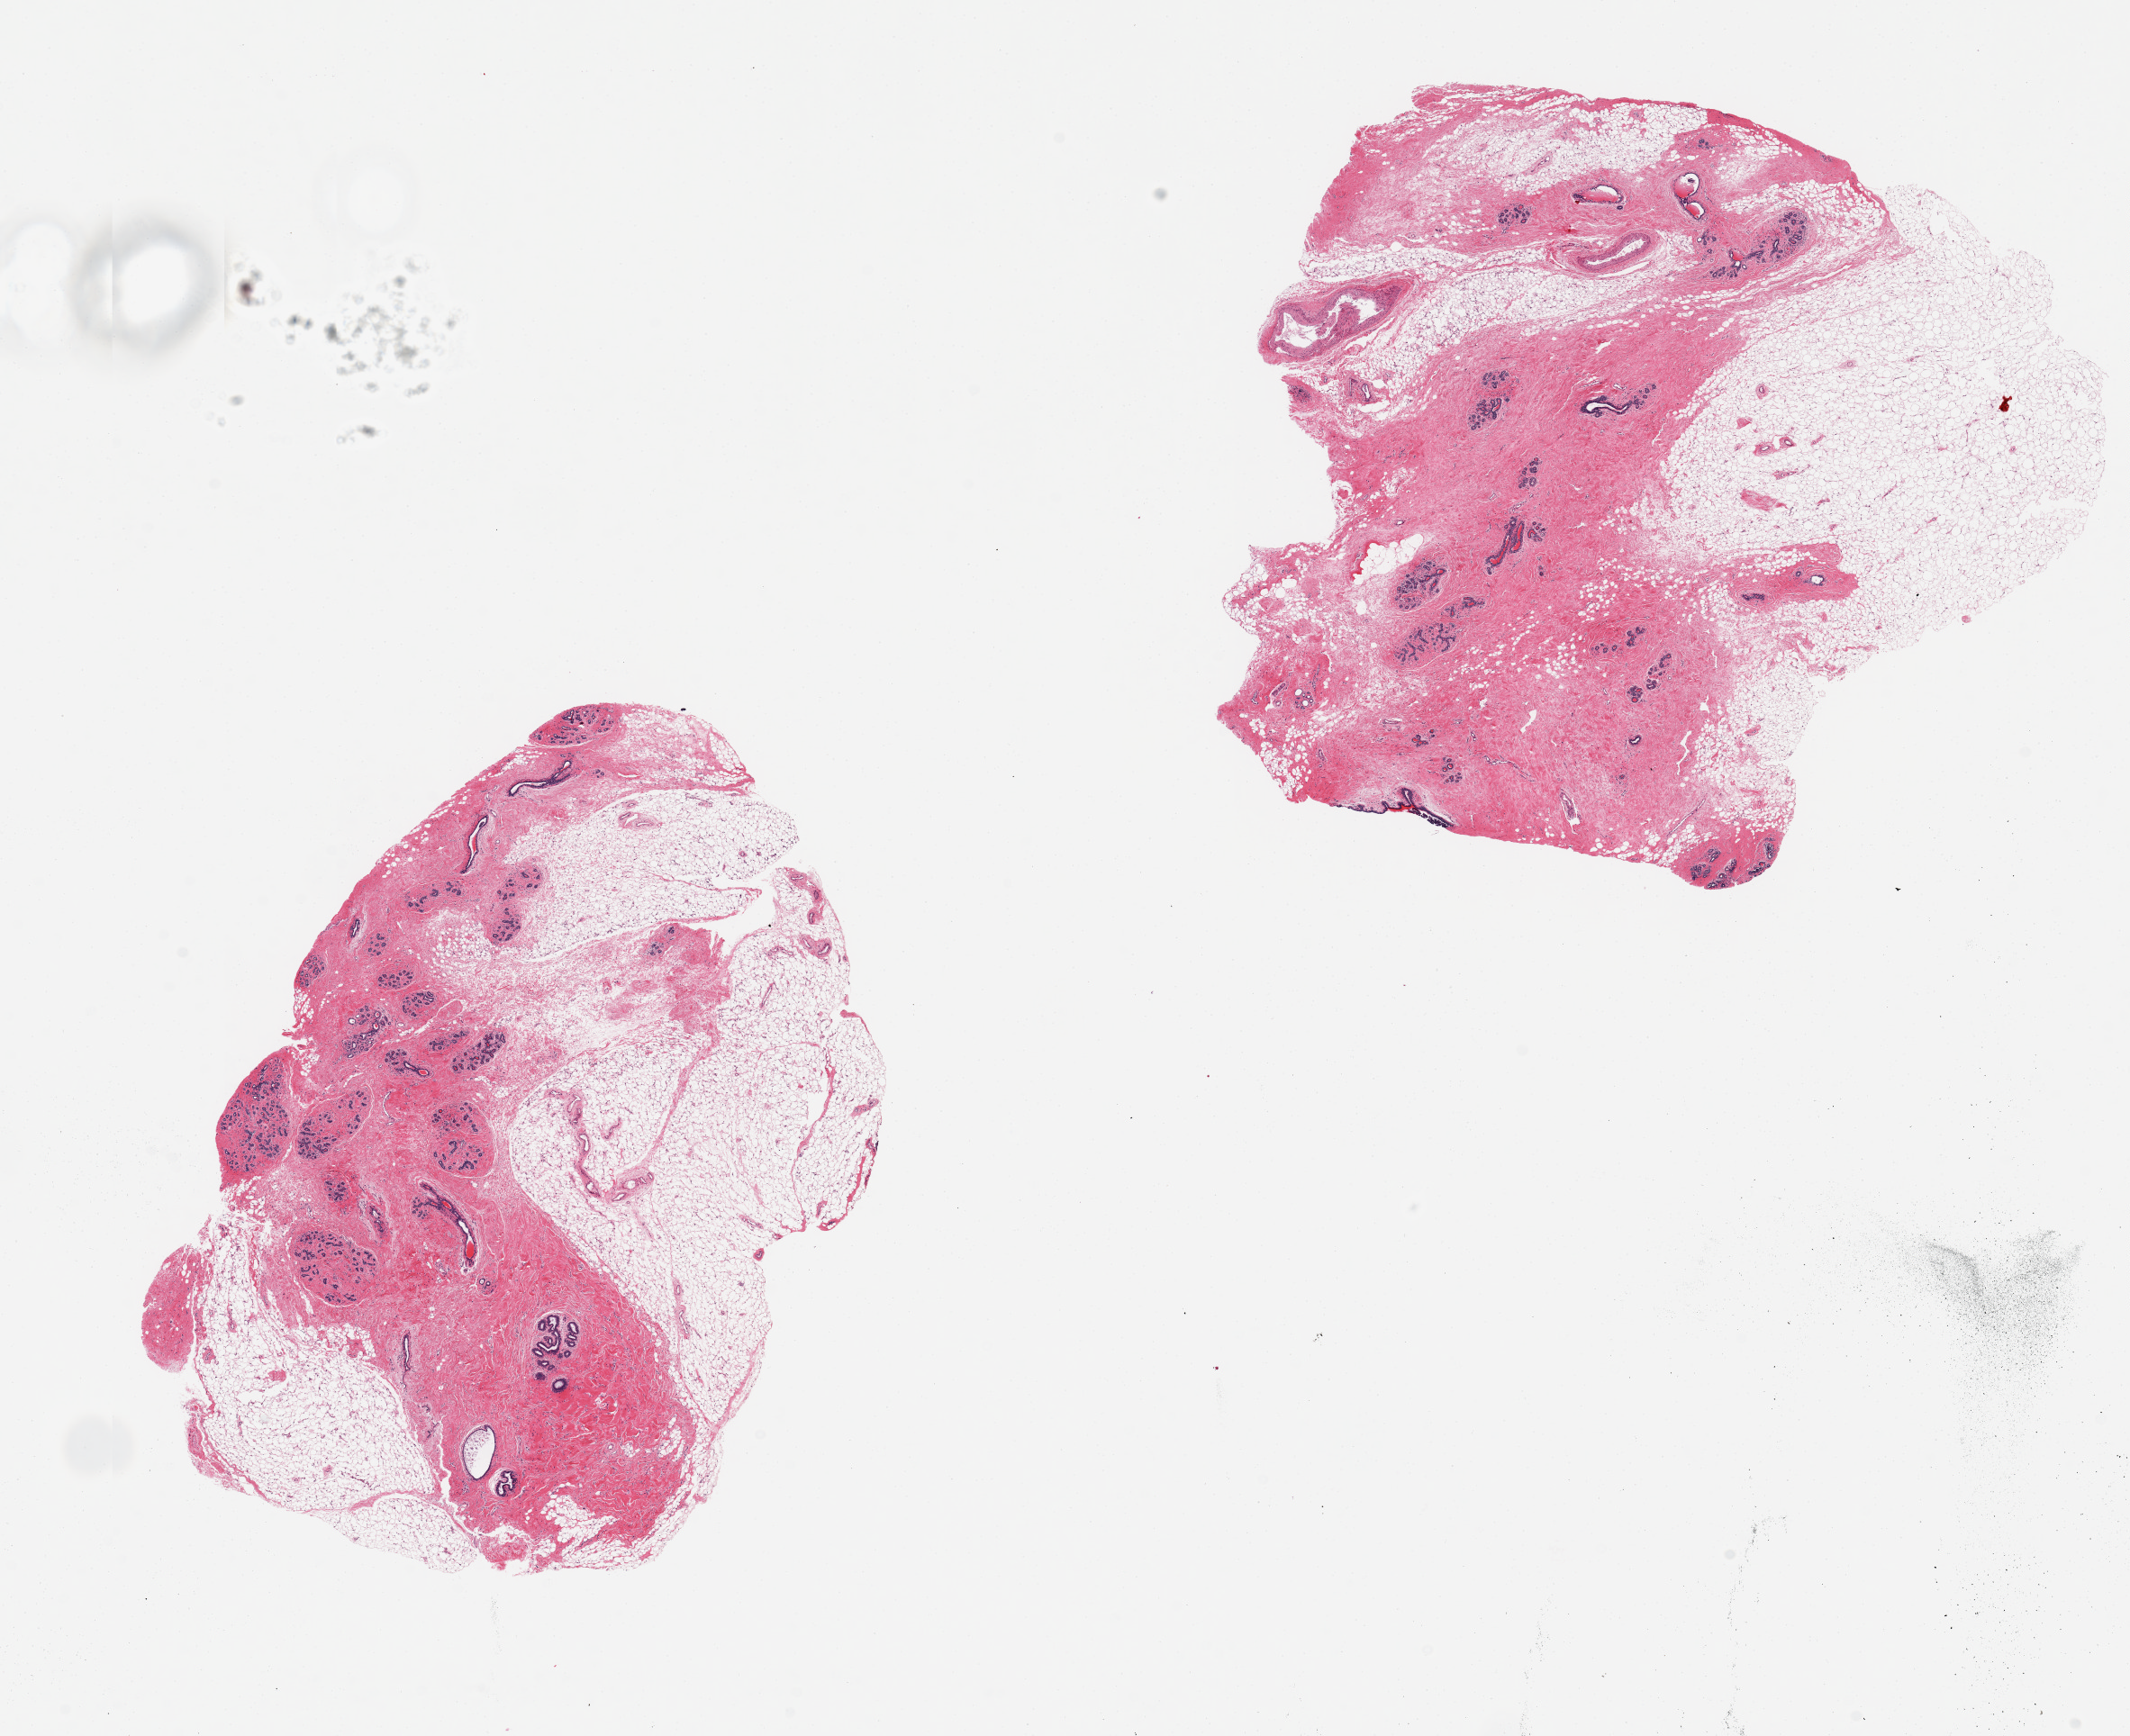
Digitized haematoxylin and eosin-stained section — shown as a low-resolution overview of the whole scanned area (about 18.7 x 15.2 mm, acquisition: 20x scan). PAXgene-fixed paraffin-embedded (PFPE) section. Section of breast (target tissue). Donor tissue sample. Donor: female.
Reviewer comment on this tissue sample: 2 aliquots, ~7x5mm. Post-menopausal TDLUs present, encricled.